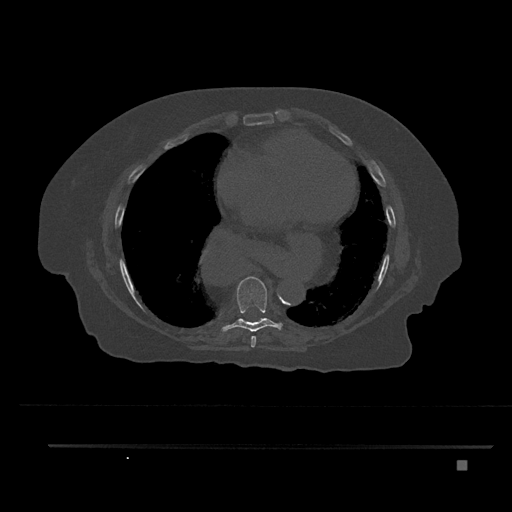
CT including the spine, one axial slice; slice 444 of 797 in the series (ordered by position); reconstruction kernel Br40s/3; 120 kVp; bone window (W 1800 / L 400 HU); 512 × 512 image matrix, field of view 437 × 437 mm. Female patient, age 76 years. Case-level facts recorded for this patient, not image findings: primary cancer: lung; vertebrae with lytic lesions (as recorded): T11, L3.
Structures marked on this image (semi-automatic segmentation, software-assisted and operator-edited):
- T7 vertebra: bounding box <251,336,256,348> (left, top, right, bottom; pixels)
- T8 vertebra: <220,277,283,333>